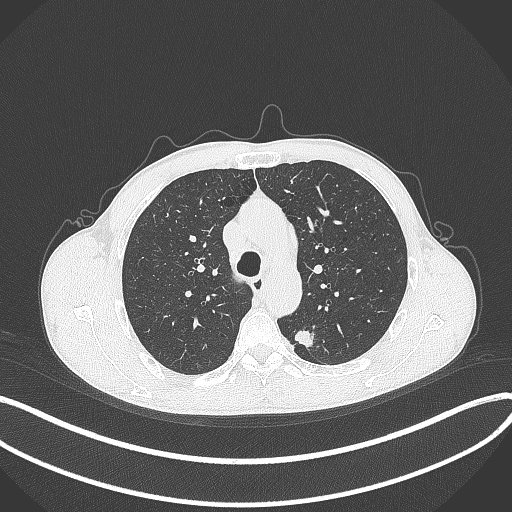
Chest CT, one axial slice. Slice 282 of 429 in the series (ordered by position). 120 kVp. Lung window (W 1500 / L -600 HU). 1 mm slice thickness. 512 × 512 image matrix, field of view 400 × 400 mm. Male patient, age 51 years. Case-level facts recorded for this patient, not image findings: clinical TNM (as recorded): T2a N1 M1.
Annotated regions visible in this slice (bounding box drawn by a radiologist):
- lung tumour (recorded histology: adenocarcinoma): bounding box (x1, y1, x2, y2) in pixels: (294, 327, 316, 353)